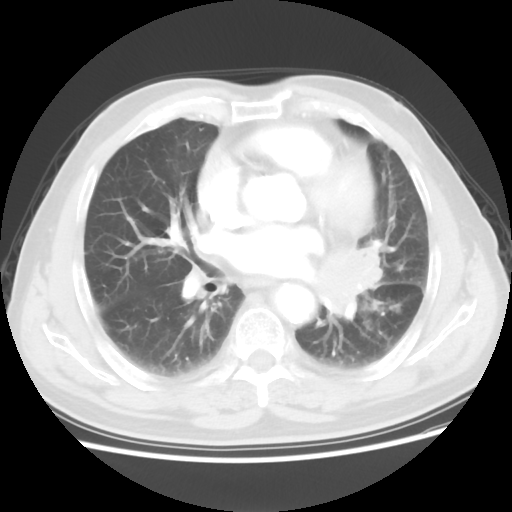
Chest CT, one axial slice. Position 29 of 56 along the scan axis. 120 kVp. Lung window (W 1500 / L -600 HU). 5 mm slice thickness. 512 × 512 image matrix, field of view 360 × 360 mm. Patient: male, 75 years. From the clinical record (not read from this slice): clinical TNM (as recorded): T3 N0 M0.
Annotated regions visible in this slice (rectangle marked by the reading radiologist):
- lung tumour (recorded histology: squamous cell carcinoma): bounding box <306,240,401,331> (left, top, right, bottom; pixels)